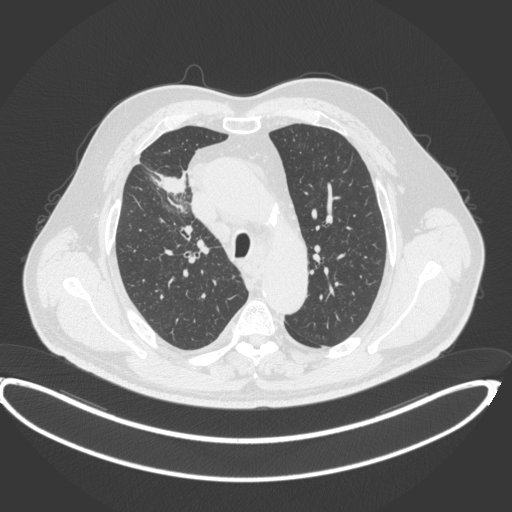
Chest CT, one axial slice. Position 297 of 395 along the scan axis. Lung window (W 1500 / L -600 HU). 1 mm slice thickness. 512 × 512 image matrix, field of view 448 × 448 mm. Patient: male, 62 years. From the clinical record (not read from this slice): clinical TNM (as recorded): T1c N3 M1c.
Structures marked on this image (rectangle marked by the reading radiologist):
- lung tumour (recorded histology: adenocarcinoma): bounding box <156,171,188,196> (left, top, right, bottom; pixels)